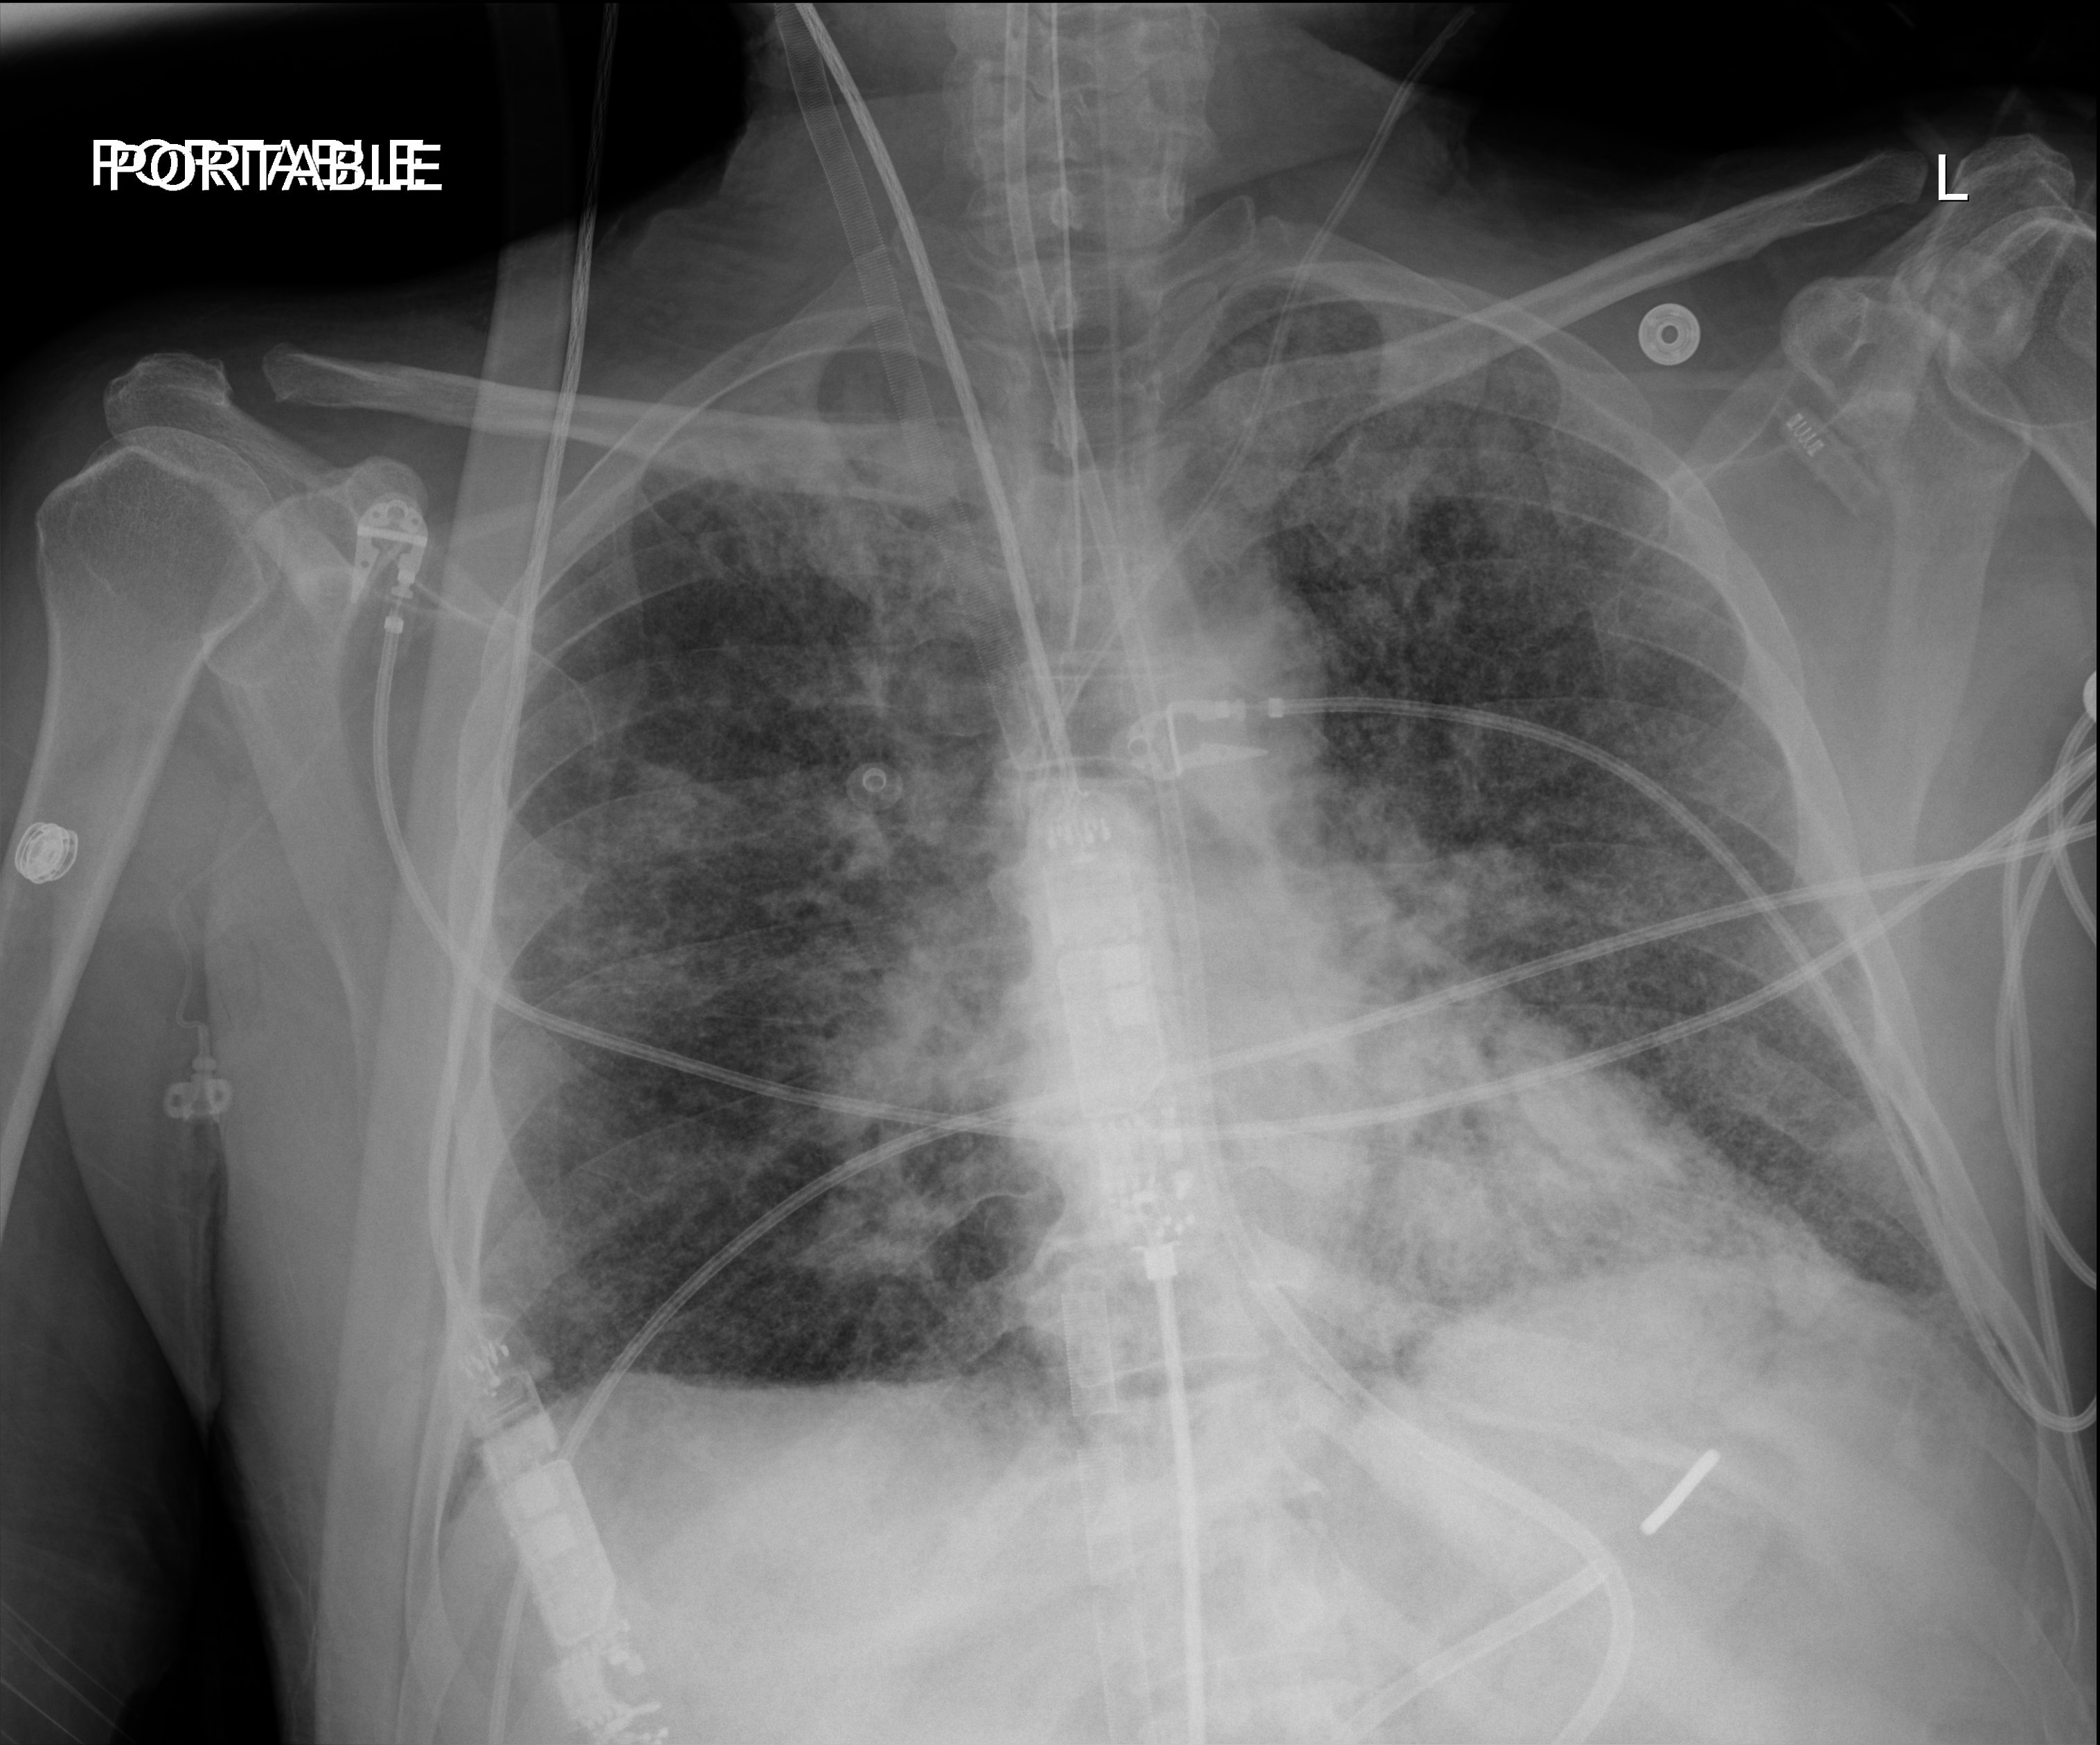
Portable chest radiograph. Patient hospitalised with COVID-19; male, aged 18–59 years.
From the hospital-stay record, not from the radiograph (when in the stay this image was taken is not recorded):
- mechanically ventilated during this hospital stay: yes
- admitted to intensive care during this hospital stay: yes